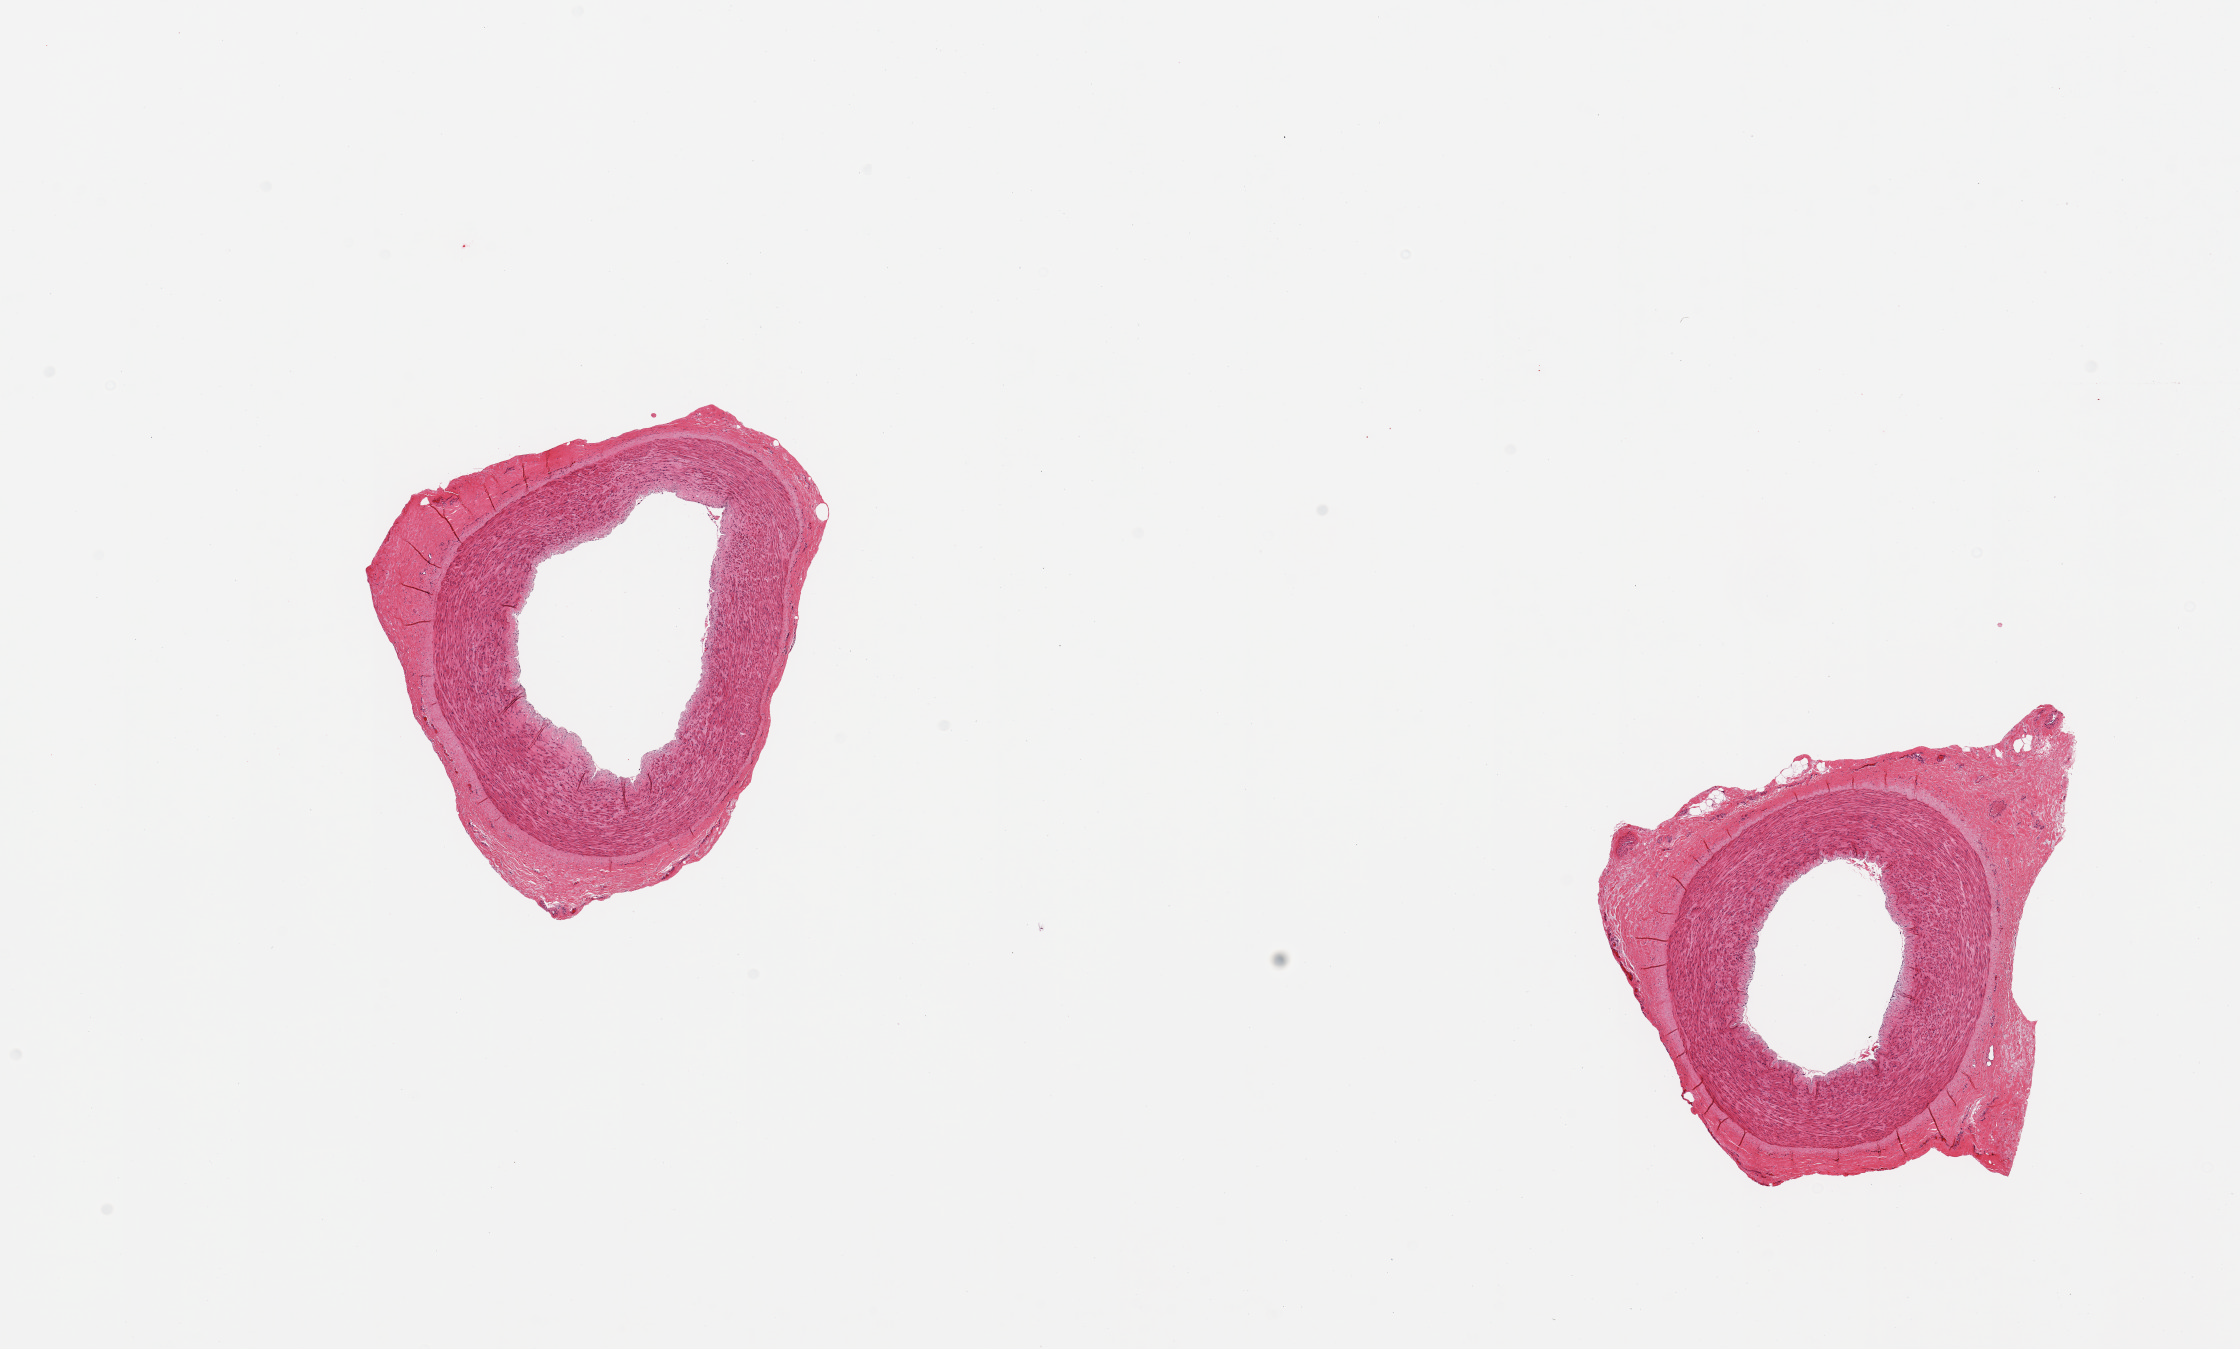
H&E whole-slide image, low-resolution overview of the scanned area, about 17.7 x 10.7 mm (from a 20x scan), PAXgene-fixed paraffin-embedded (PFPE) section, section of tibial artery (target tissue), tissue donor sample. Donor sex: male.
Review note (as recorded): 2 pieces; no plaques; well trimmed.